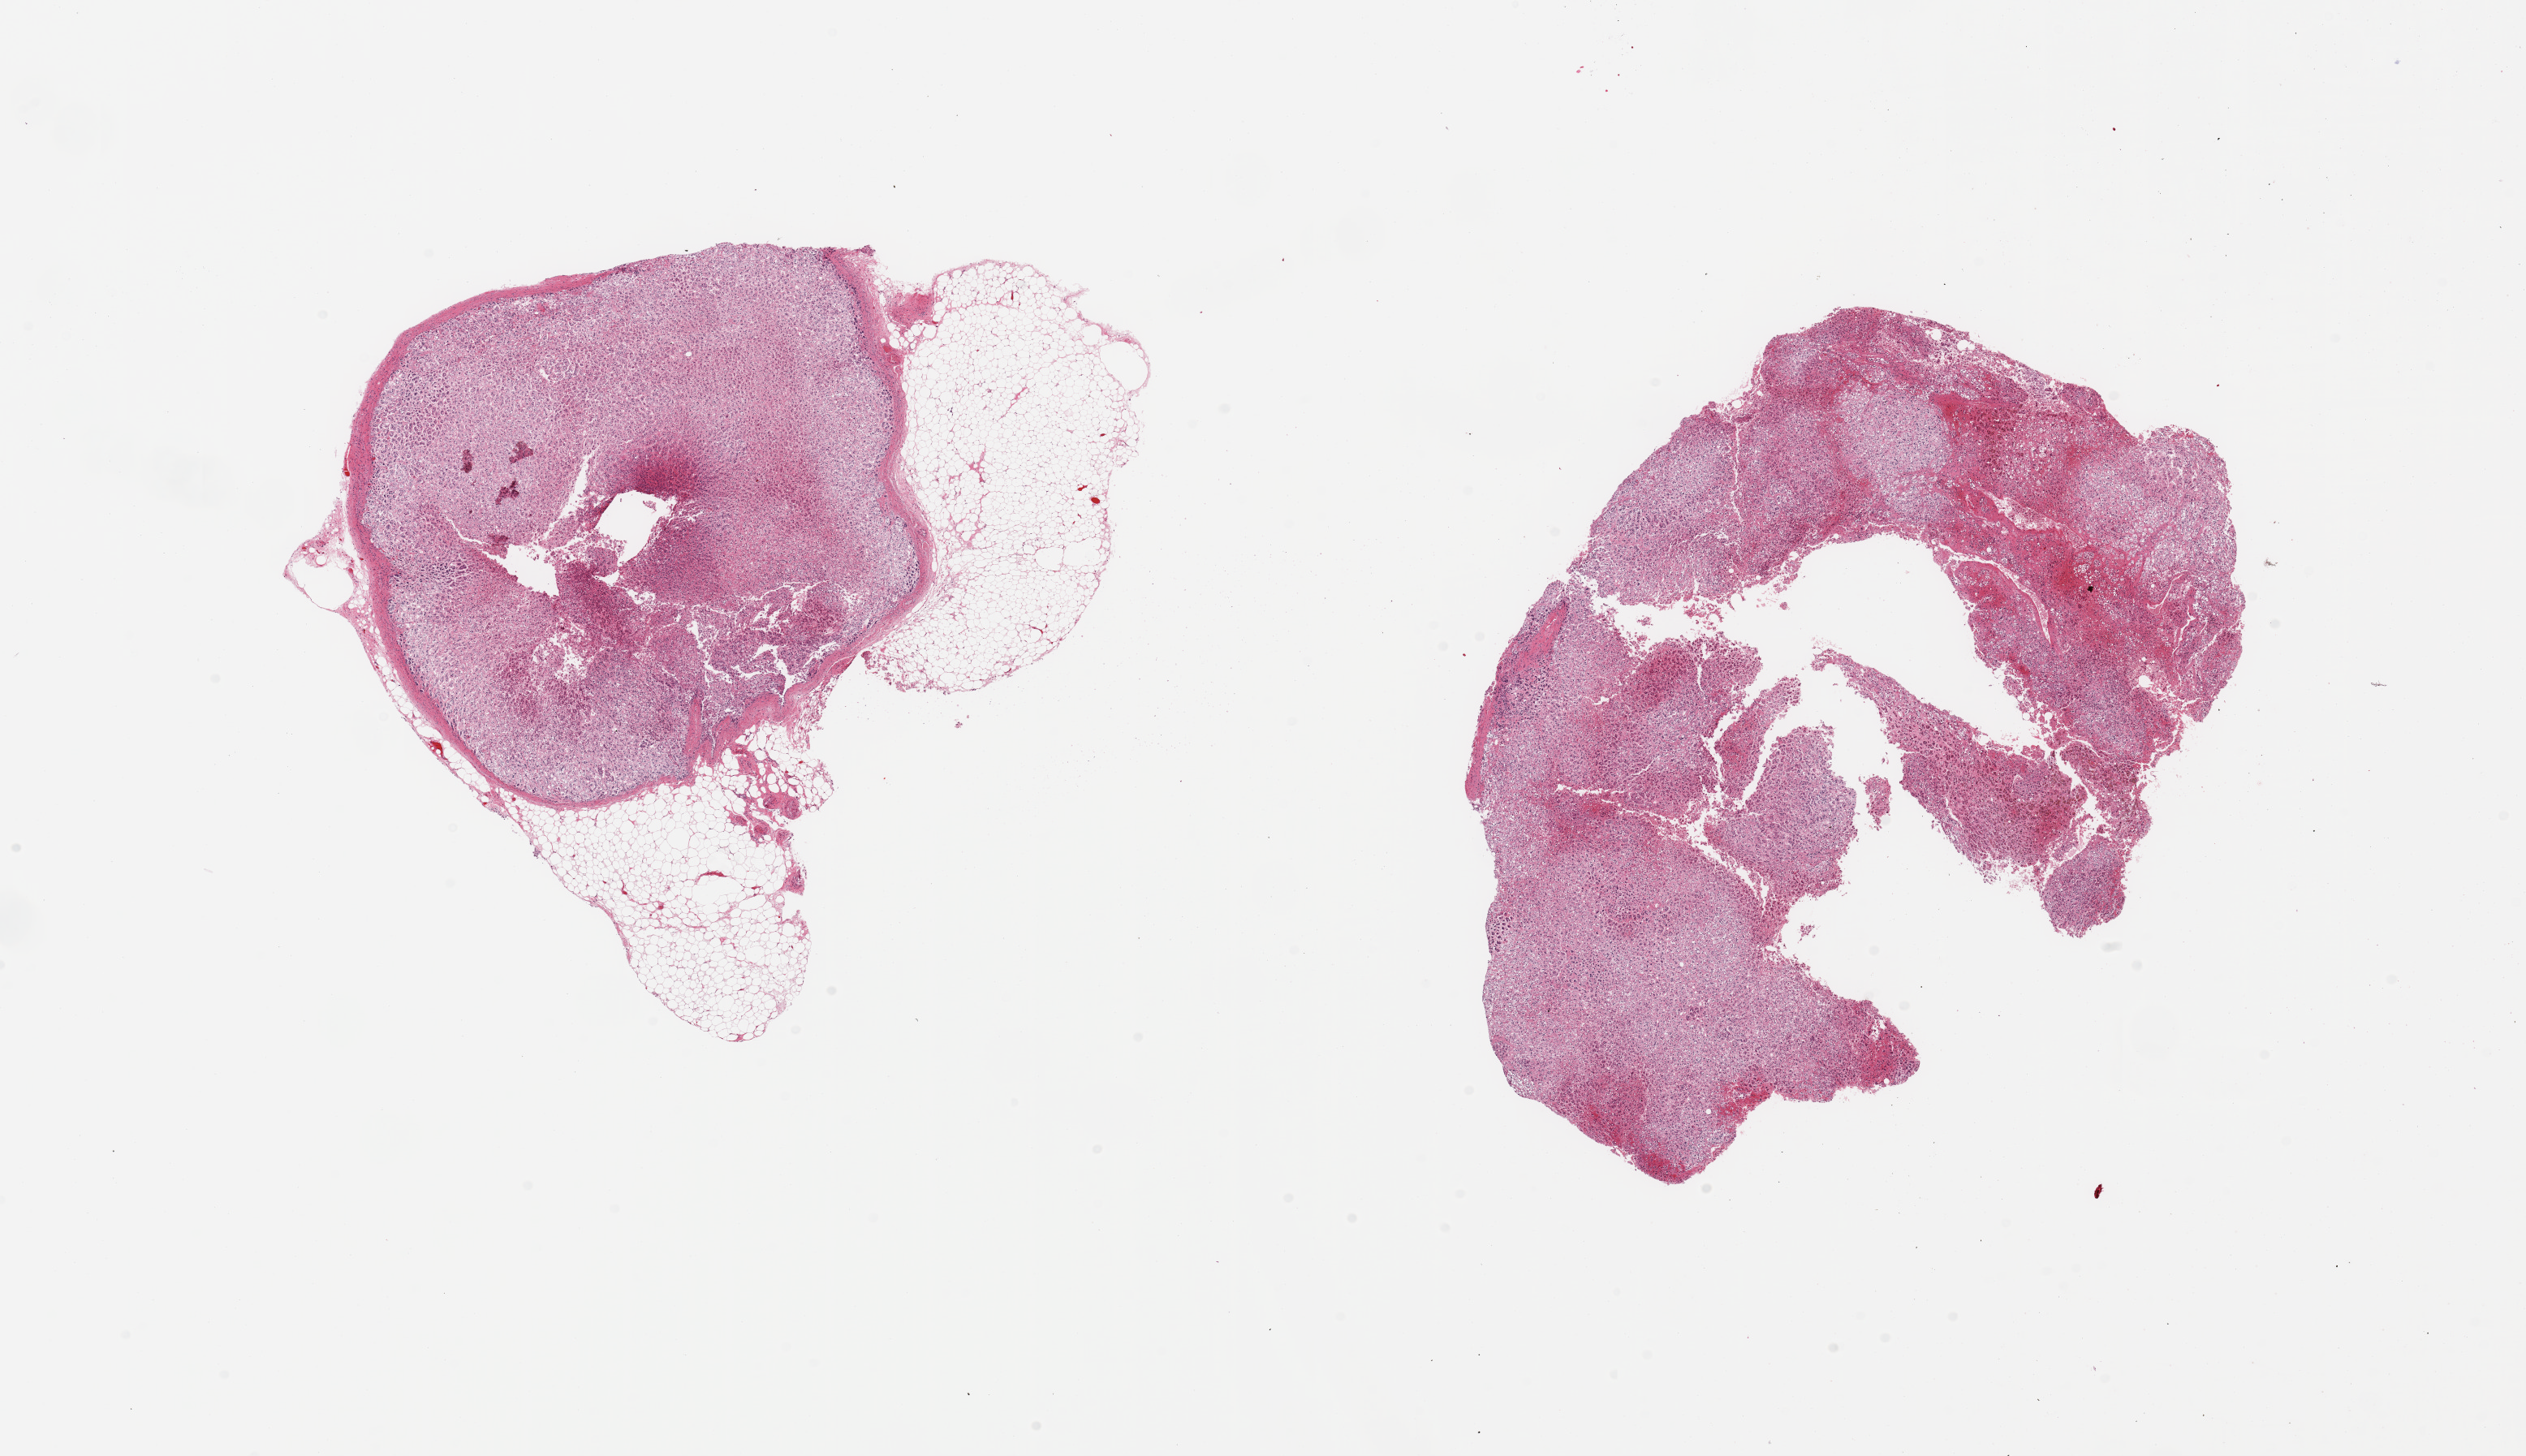
Hematoxylin and eosin (H&E) whole-slide image, a low-resolution overview of the entire scanned area, about 24.6 x 14.2 mm (slide scanned at 20x); PAXgene-fixed, paraffin-embedded tissue; section of adrenal gland (target tissue); donor tissue sample.
* review note (as recorded): 2 pieces, cortex, adherent fatty nubbins up to ~2.5mm